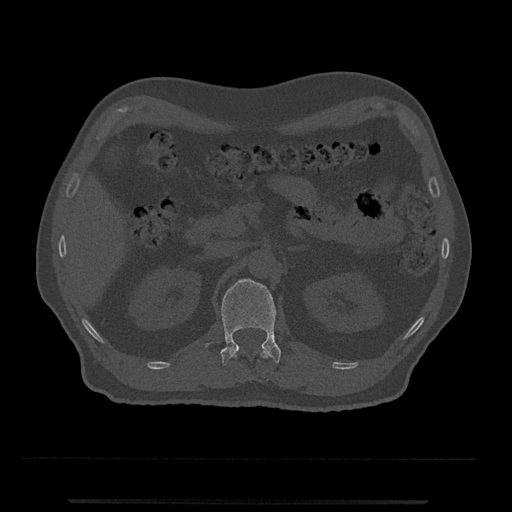
CT including the spine, one axial slice; slice 354 of 797 in the series (ordered by position); 120 kVp; bone window (W 1800 / L 400 HU); 0.5 mm slice thickness; 512 × 512 image matrix, field of view 419 × 419 mm. Patient: male, 63 years. From the clinical record (not read from this slice): primary cancer: prostate.
Annotated regions visible in this slice (semi-automatically segmented with operator editing):
- L1 vertebra: bounding box (x1, y1, x2, y2) in pixels: (206, 278, 281, 366)
- T12 vertebra: (233, 347, 270, 358)